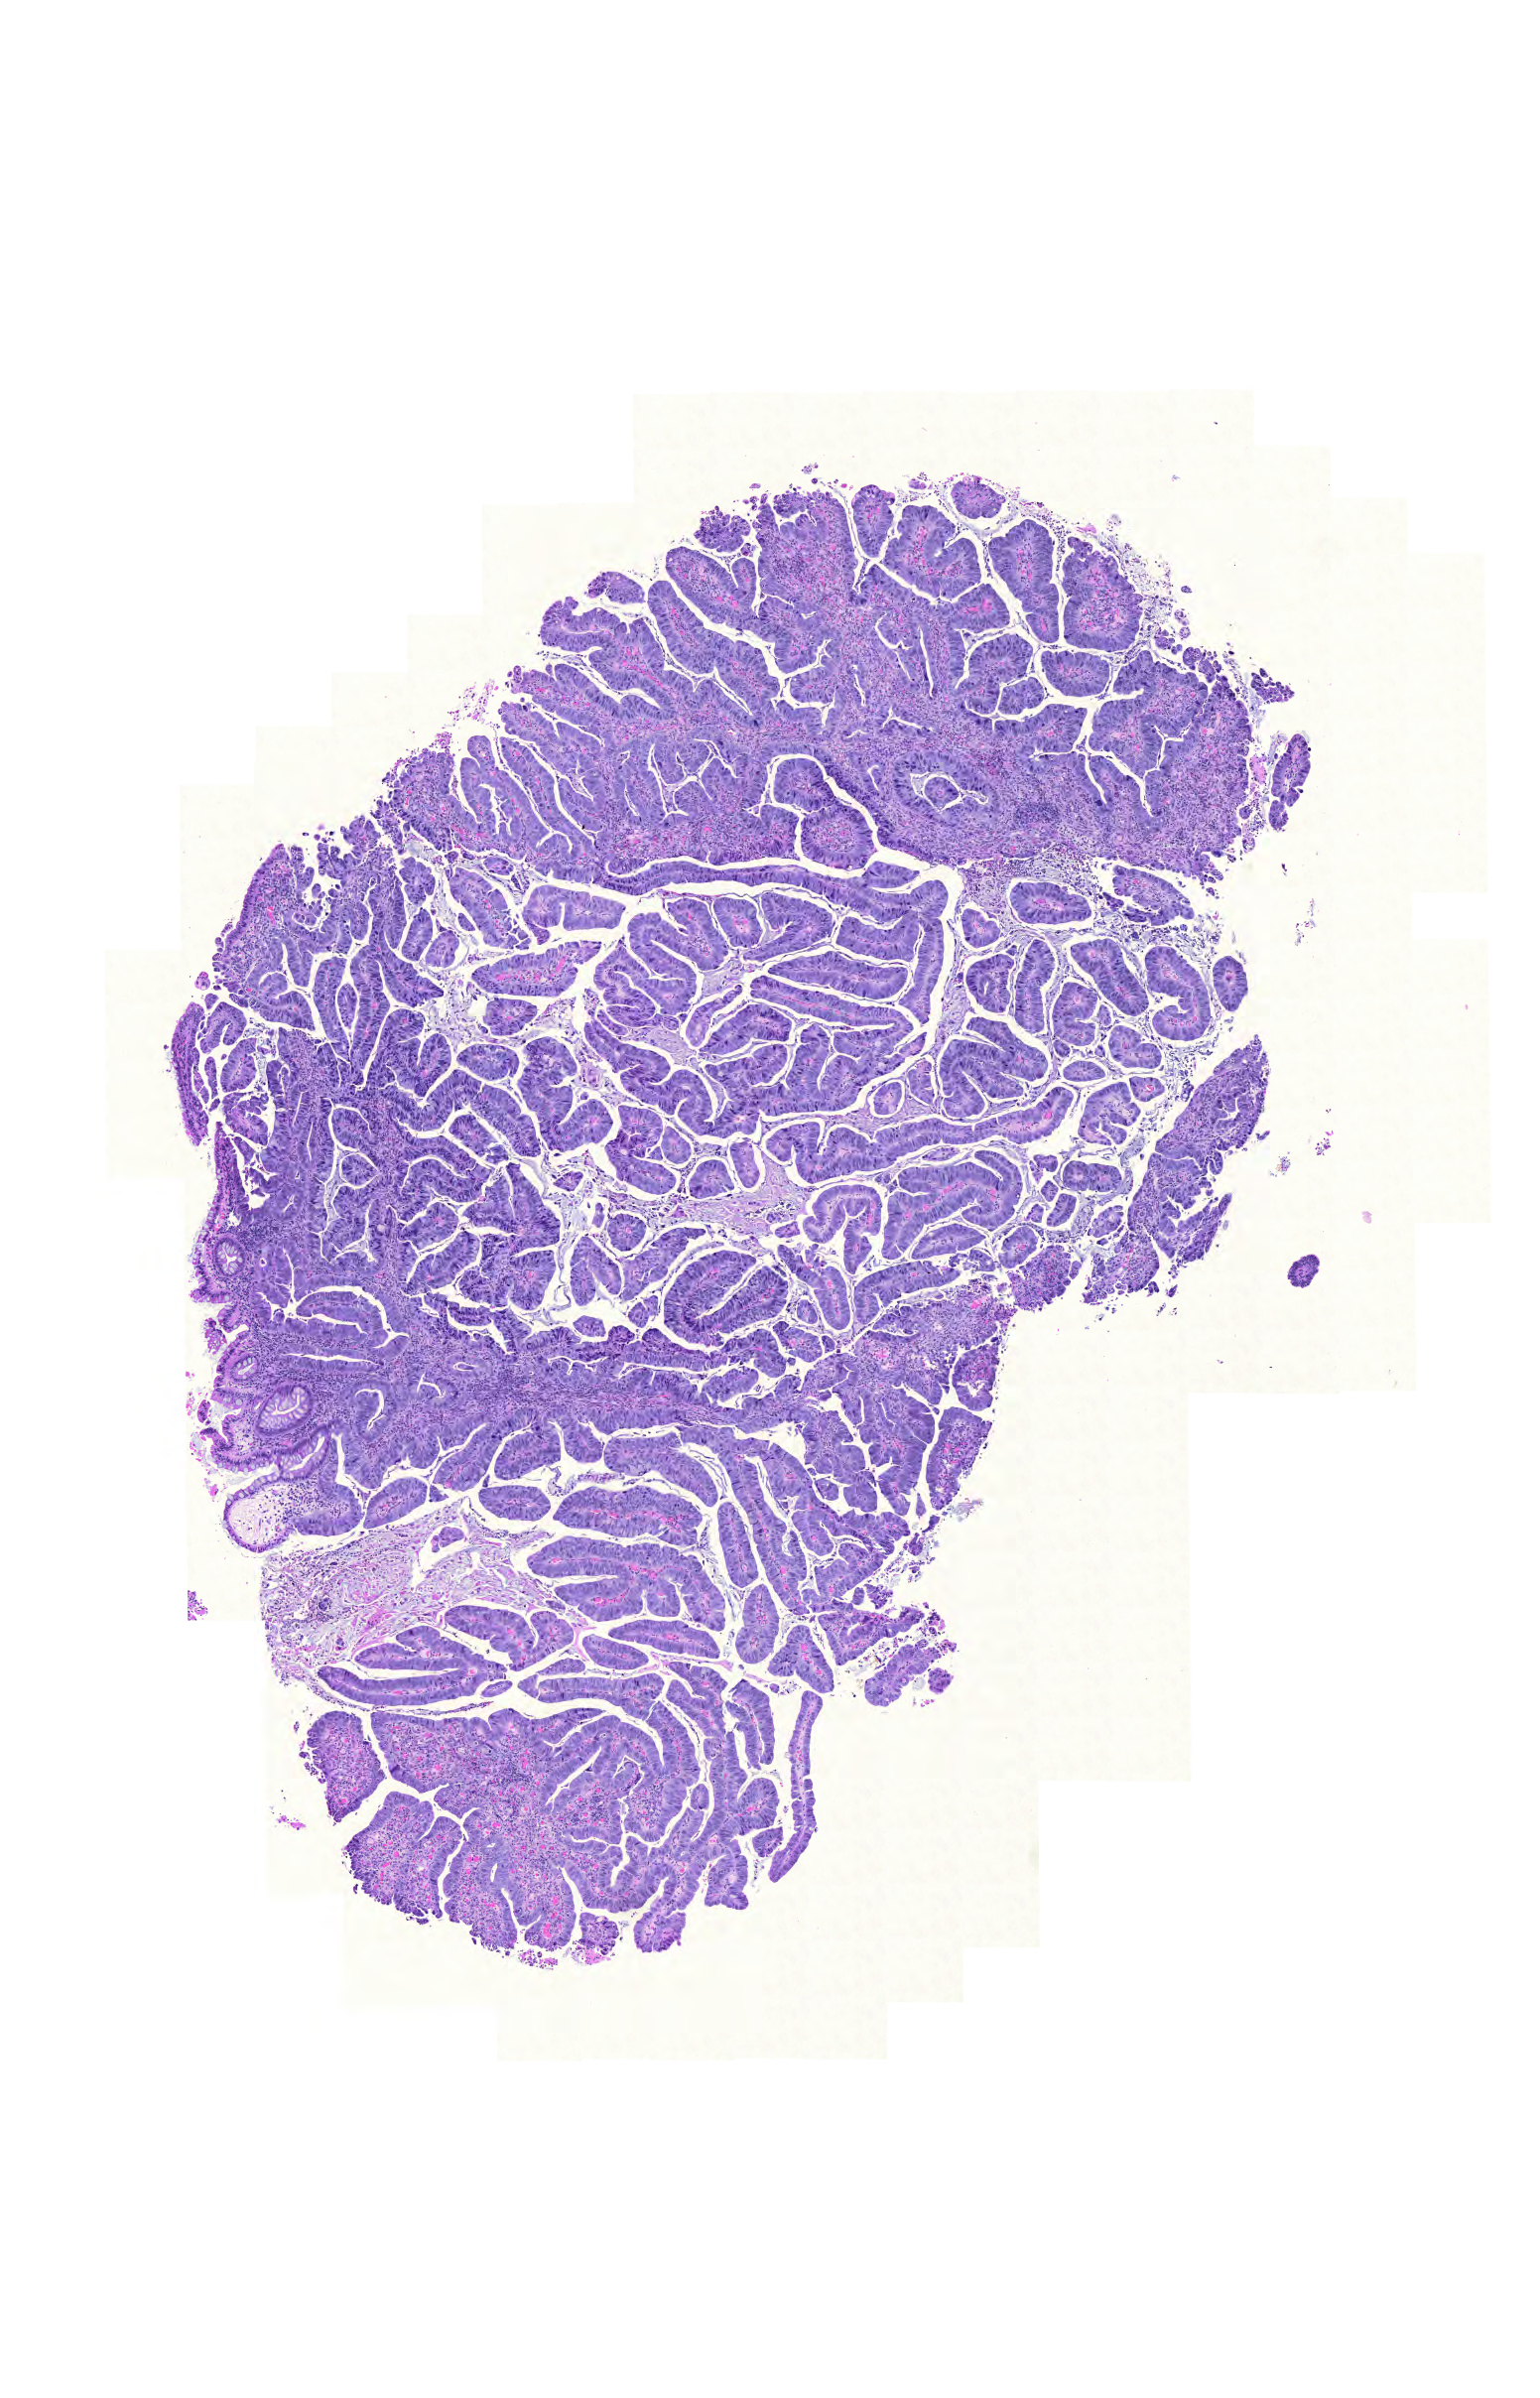
Digitized H&E-stained tissue section (whole slide) — whole scanned area (about 5.8 x 9.0 mm, from a 20x scan) shown as a low-resolution overview. Formalin-fixed paraffin-embedded (FFPE) diagnostic section. Sample: primary tumour, colon. Male, age 78 years at initial diagnosis.
AJCC pathologic stage: I (6th edition). Pathologic diagnosis: Mucinous adenocarcinoma (sigmoid colon). Lymph nodes positive (case pathology): 0 of 22 examined. TNM: T2 N0 M0.